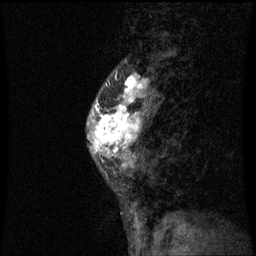
Breast MRI (dynamic contrast-enhanced), one sagittal slice. Position 25 of 60 along the scan axis. Dynamic contrast-enhanced series, image 2 of 3 at this slice position (ordered by acquisition). 1.5 T. TE 4.2 ms, TR 8.9 ms. 2 mm slice thickness. 256 × 256 image matrix, field of view 200 × 200 mm. Female patient, age 50 years. From the clinical record (not read from this slice): setting: breast cancer imaged before/during neoadjuvant chemotherapy; receptor status: triple-negative.
Structures marked on this image (semi-automatically segmented with operator editing):
- analysis volume of interest (the breast-tissue region the enhancement analysis was run in; not a lesion): bounding box <88,80,155,171> (left, top, right, bottom; pixels)
- tumour enhancement mask (voxels above the 70 % enhancement threshold inside the analysis volume of interest): <94,80,147,167>